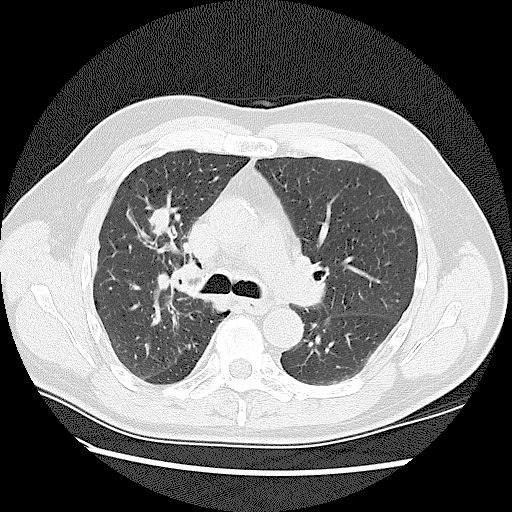
Low-dose screening chest CT, one axial slice. Slice 80 of 128 in the series (ordered by position). 120 kVp. Lung window (W 1500 / L -600 HU). 2.5 mm slice thickness. 512 × 512 image matrix.
Outlined on this slice (manually delineated by an expert):
- lesion 1 (tumor, upper lobe of right lung): bounding box [x1, y1, x2, y2] px = [148, 208, 170, 235]